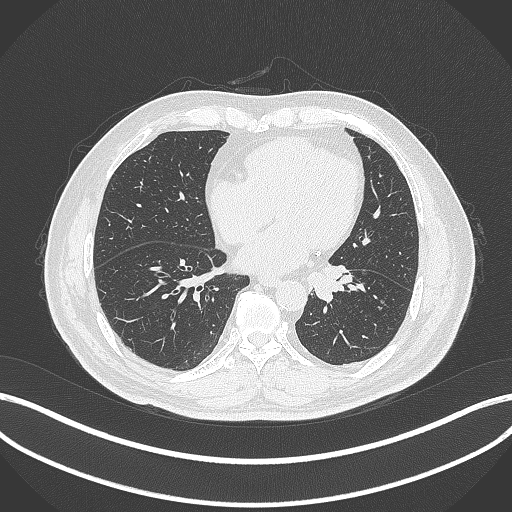
Chest CT, one axial slice. Position 101 of 312 along the scan axis. Reconstruction kernel B70f. Lung window (W 1500 / L -600 HU). 1 mm slice thickness. 512 × 512 image matrix, field of view 400 × 400 mm. Male patient, age 71 years. From the clinical record (not read from this slice): clinical TNM (as recorded): T1b N0 M0.
Annotated regions visible in this slice (rectangle marked by the reading radiologist):
- lung tumour (recorded histology: squamous cell carcinoma): bounding box [x1, y1, x2, y2] px = [304, 261, 352, 304]